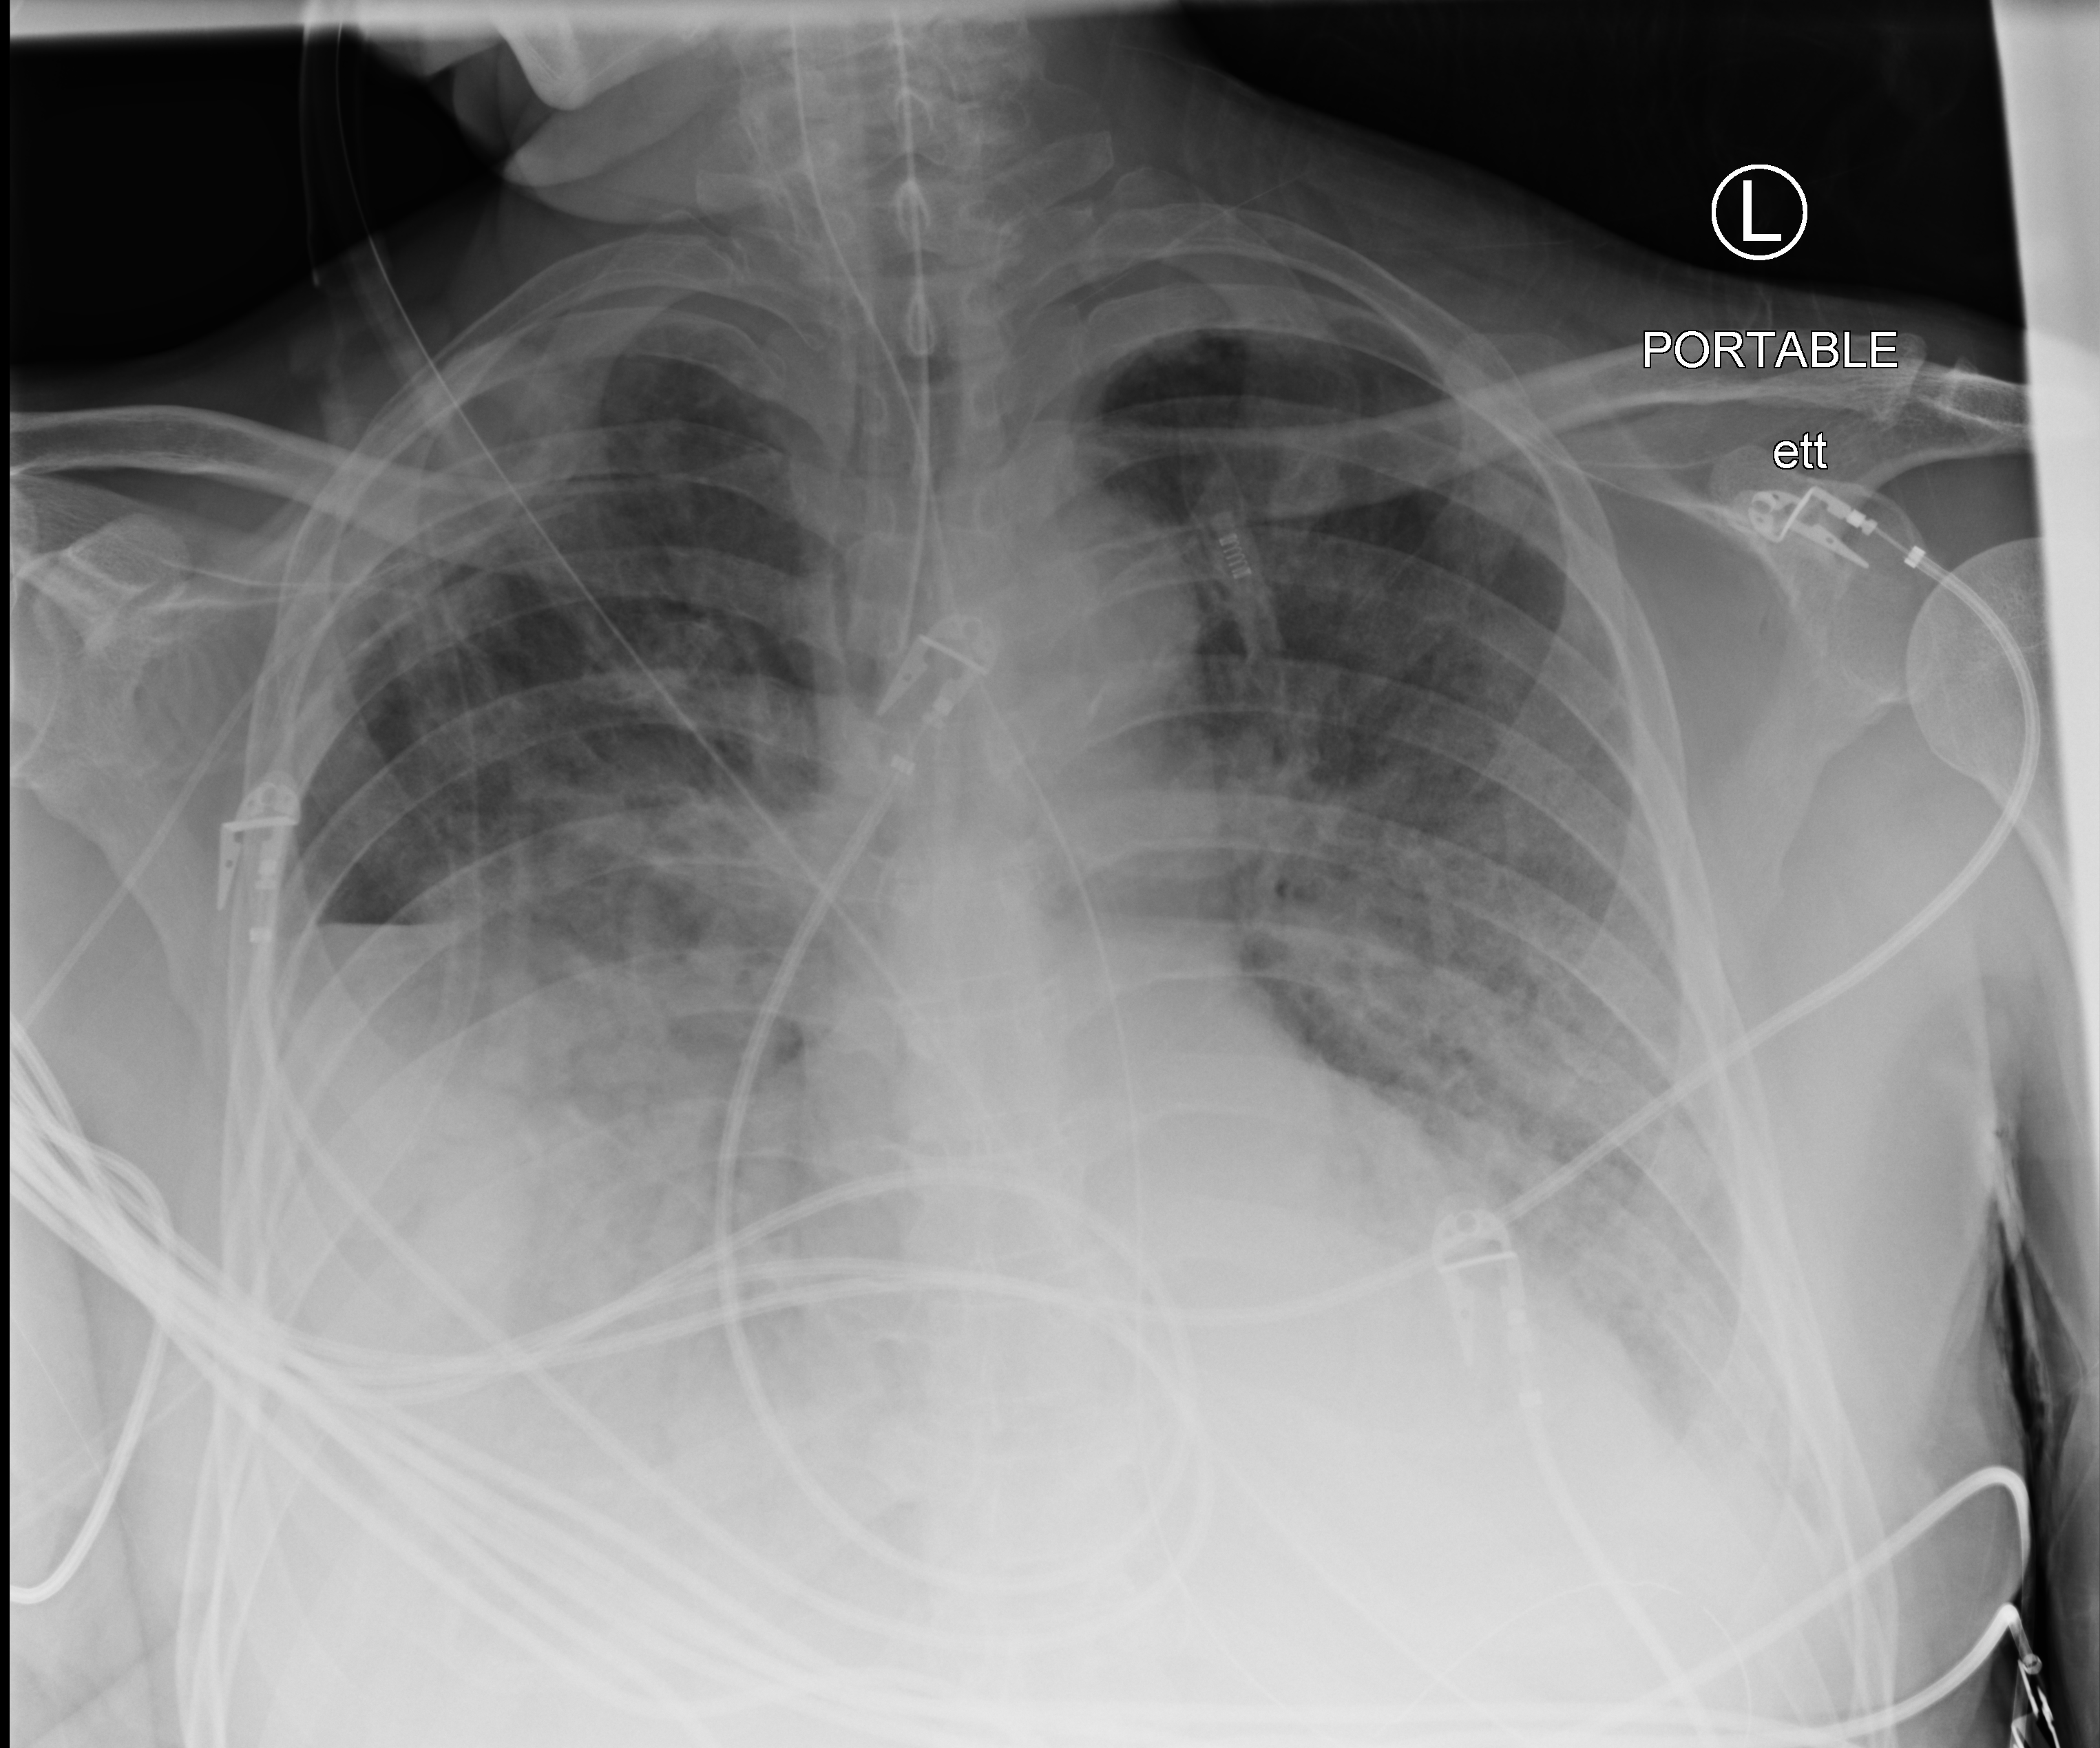
Portable chest radiograph; anteroposterior (AP) projection. Patient hospitalised with COVID-19; male, aged 60–74 years.
Admission-level facts for this patient (not findings on this image; timing relative to this image not recorded): diabetes (admission record): no; hypertension (admission record): no; length of hospital stay: 31 days.